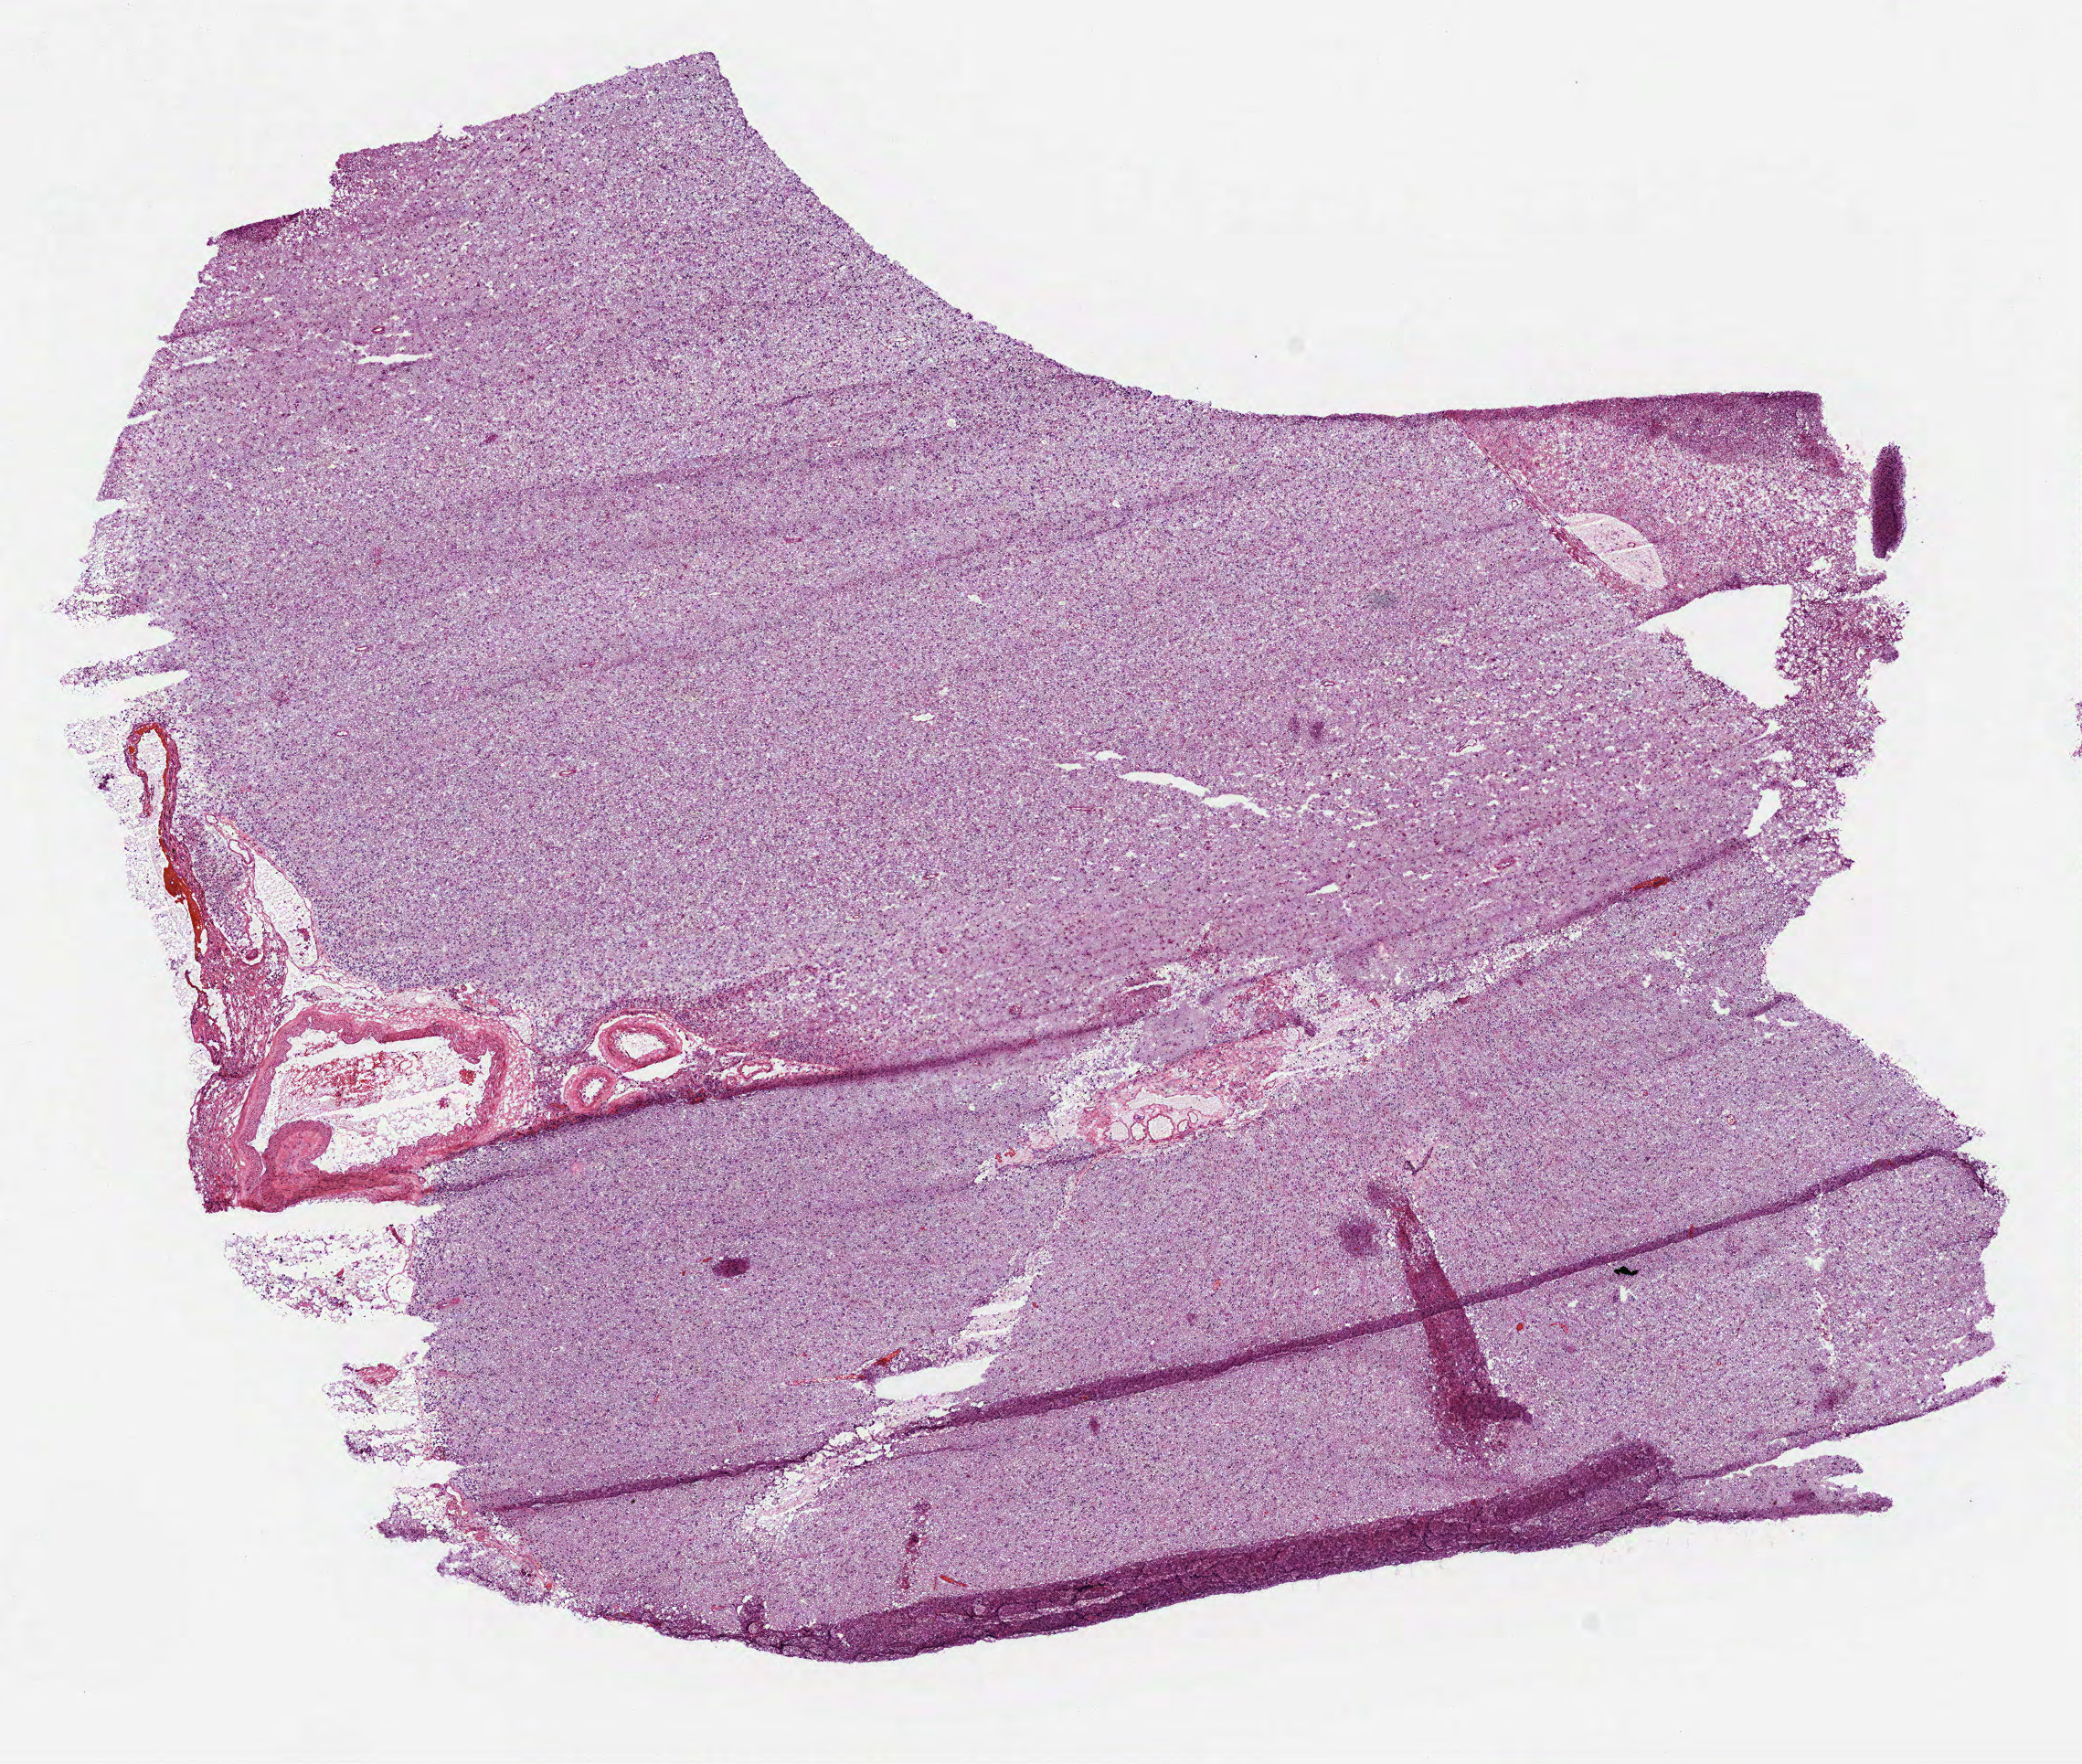
H&E-stained whole-slide image, low-resolution overview of the scanned area, about 9.2 x 7.8 mm (slide scanned at 40x), frozen section from the bottom of the tissue portion, sample: primary tumour, brain. Patient: female, age at initial diagnosis 48 years. Histologic grade: G3 (poorly differentiated). Pathologist review of this section (percent, as recorded): tumour cells 100%, tumour nuclei 65%, normal cells 0%, stromal cells 0%, necrosis 0%.
Laterality: left. Diagnosis: Oligodendroglioma, anaplastic (cerebrum).